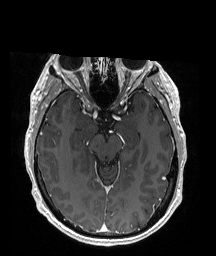
Brain MRI from a brain-tumour surgery series, one axial slice; position 114 of 176 along the scan axis; T1-weighted post-contrast; 1 mm slice thickness; 216 × 256 image matrix. Case-level facts recorded for this patient, not image findings: histopathology: Oligodendroglioma; WHO grade: 2; IDH mutation: yes.
Annotated regions visible in this slice (manually delineated by an expert):
- tumour: bounding box <88,150,93,157> (left, top, right, bottom; pixels)